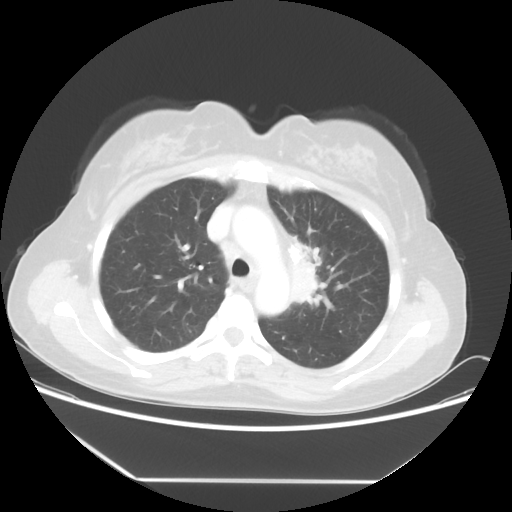
Chest CT, one axial slice. Position 37 of 52 along the scan axis. Reconstruction kernel STANDARD. Lung window (W 1500 / L -600 HU). 5 mm slice thickness. 512 × 512 image matrix, field of view 390 × 390 mm. Female patient, age 50 years. Case-level facts recorded for this patient, not image findings: clinical TNM (as recorded): T2 N3 M0.
Structures marked on this image (bounding box drawn by a radiologist):
- lung tumour (recorded histology: adenocarcinoma): bounding box <281,229,331,316> (left, top, right, bottom; pixels)